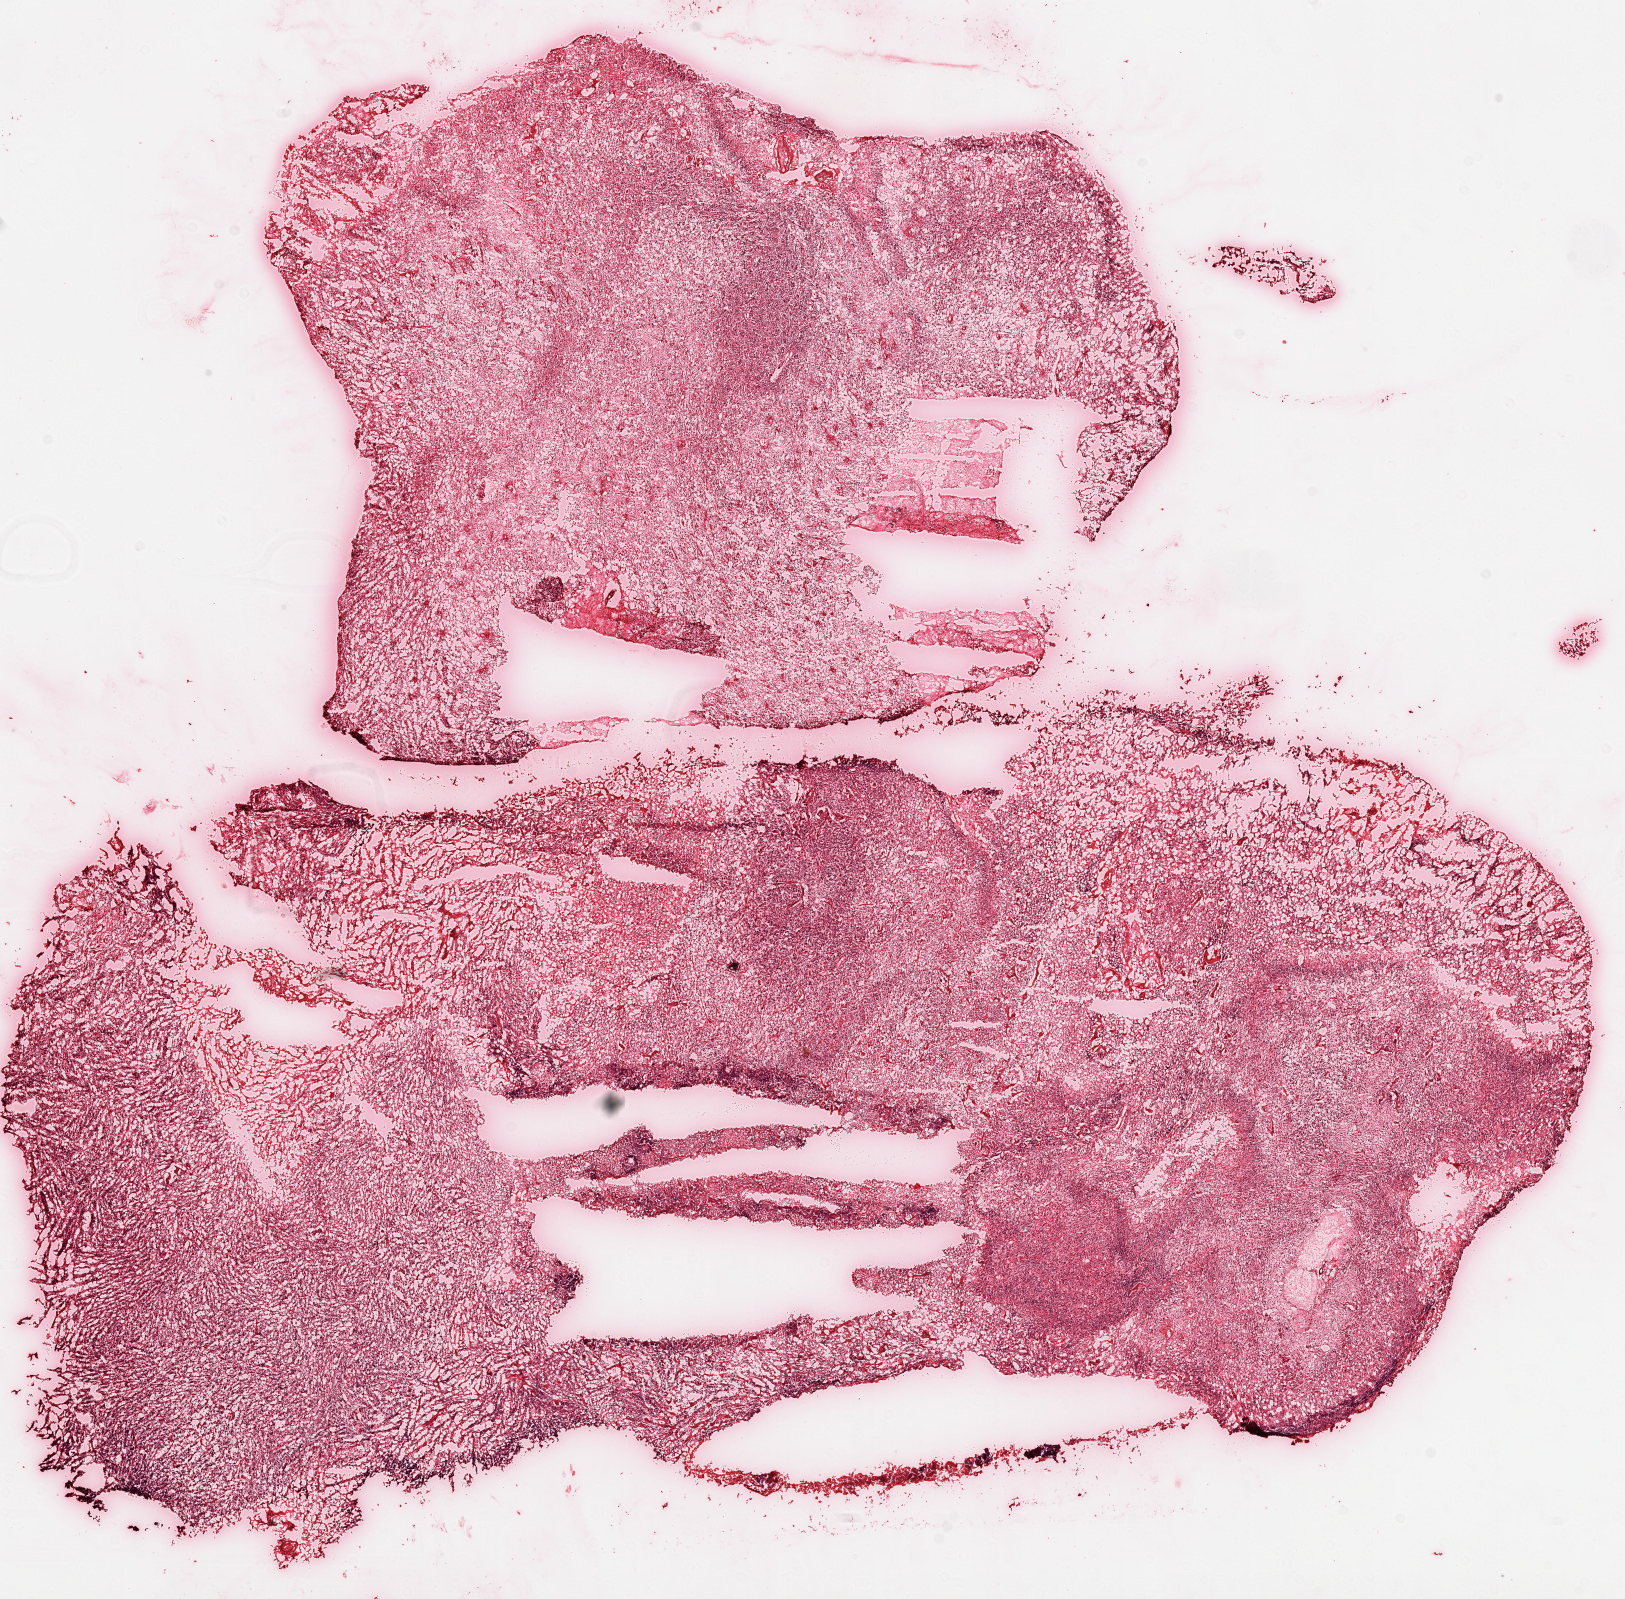
H&E whole-slide image — a low-resolution overview of the entire scanned area, about 13.0 x 12.8 mm (acquisition: 20x scan). Frozen section from the top of the tissue portion. Sample: primary tumour, brain. Female, age 50 years at initial diagnosis. Composition of this section per pathologist review: tumour cells 90%, tumour nuclei 100%, normal cells 0%, stromal cells 0%, necrosis 10%.
- diagnosis: Glioblastoma